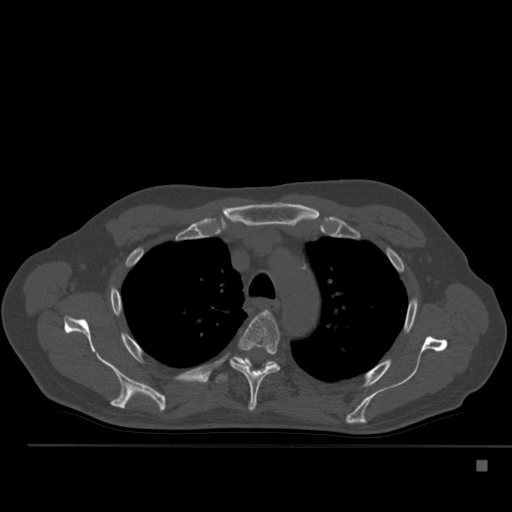
CT including the spine, one axial slice. Slice 379 of 517 in the series (ordered by position). Bone window (W 1800 / L 400 HU). 1.5 mm slice thickness. 512 × 512 image matrix, field of view 408 × 408 mm. Patient: male, 70 years. Case-level facts recorded for this patient, not image findings: primary cancer: renal; vertebrae with lytic lesions (as recorded): T4, T6, T10, T12, L3, L4, L5.
Structures marked on this image (semi-automatic segmentation, software-assisted and operator-edited):
- T4 vertebra: bounding box (x1, y1, x2, y2) in pixels: (230, 311, 280, 411)
- T5 vertebra: (215, 356, 275, 383)